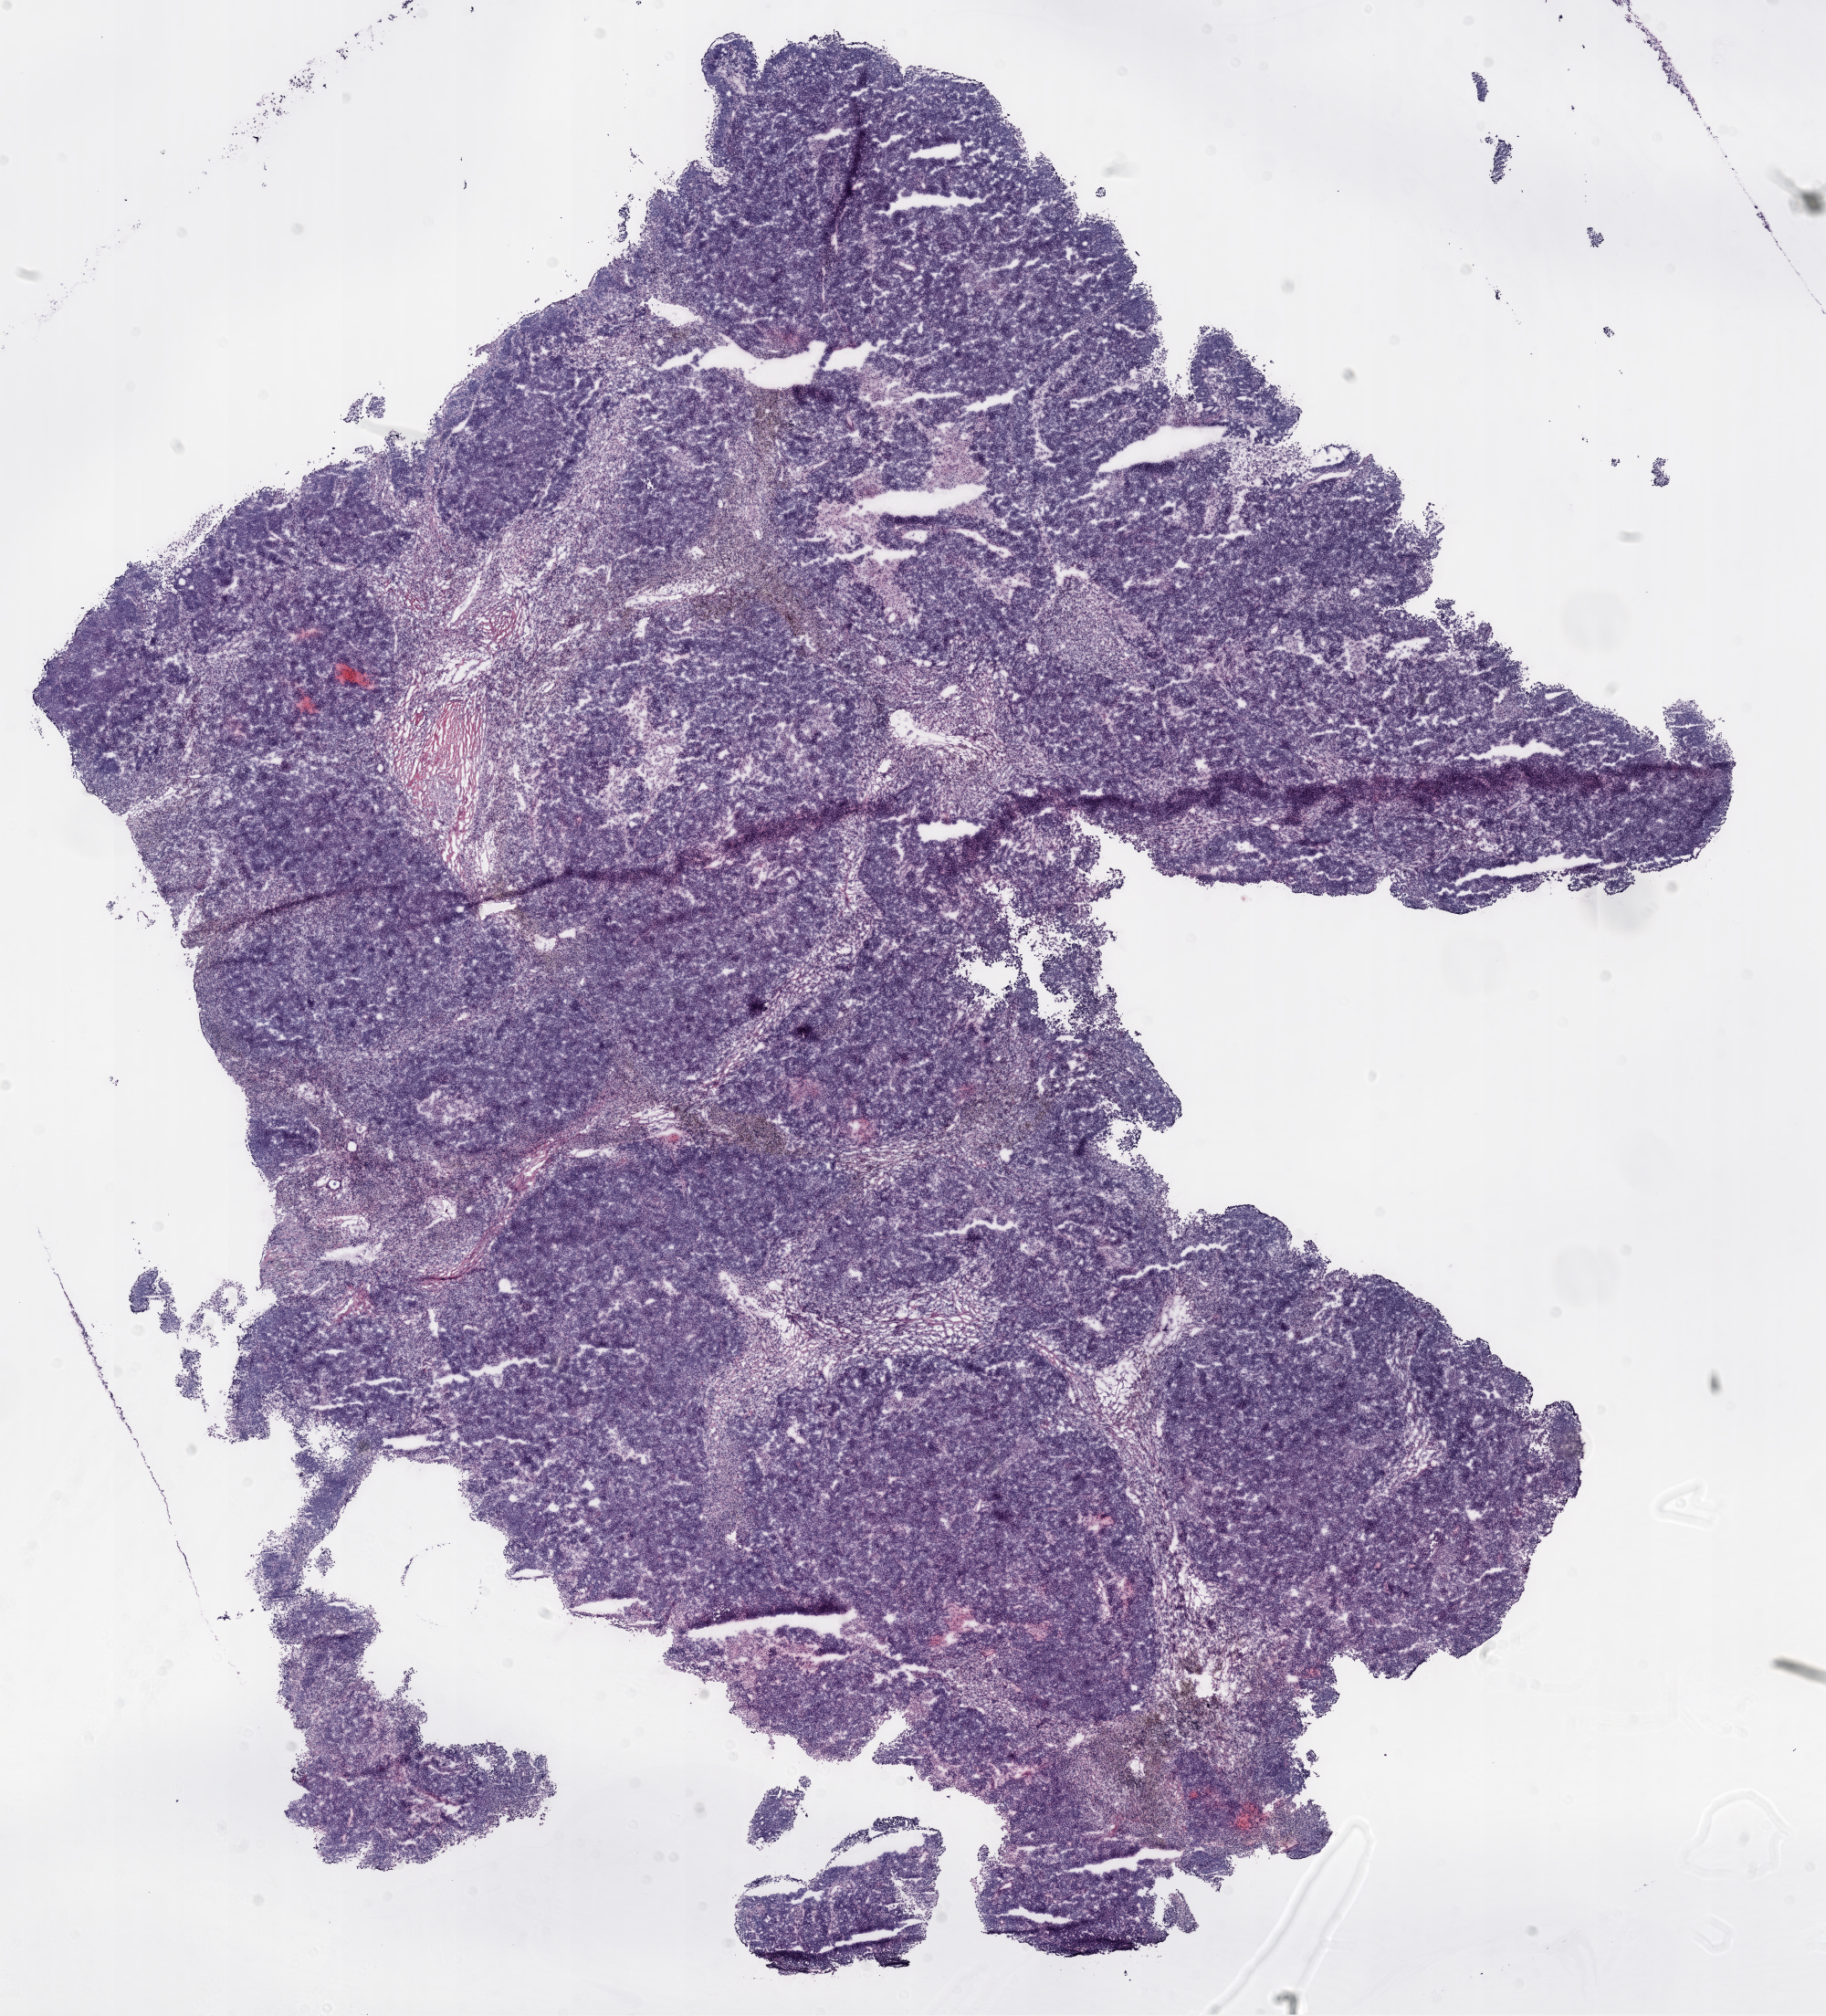
H&E whole-slide image, low-resolution overview of the scanned area, about 16.0 x 17.7 mm (from a 20x scan); frozen section from the top of the tissue portion; primary tumour sample from the ovary. Female patient; age at initial diagnosis 56 years. Histologic grade: G3 (poorly differentiated). Composition of this section per pathologist review: tumour cells 90%, tumour nuclei 90%, normal cells 0%, stromal cells 10%, necrosis 0%.
FIGO stage: IIIC. Histologic diagnosis: Serous cystadenocarcinoma, NOS.